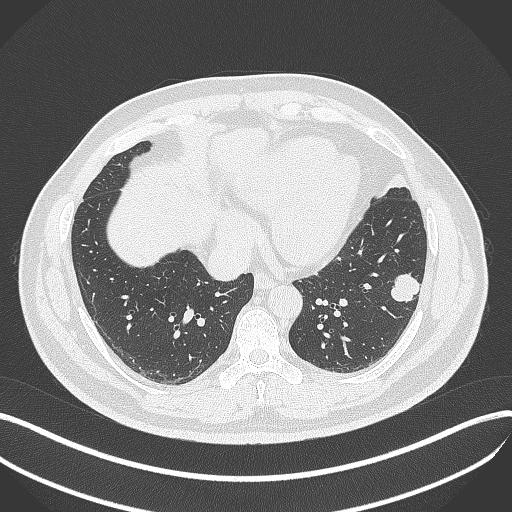
Chest CT, one axial slice. Reconstruction kernel B70f. Lung window (W 1500 / L -600 HU). 1 mm slice thickness. 512 × 512 image matrix, field of view 400 × 400 mm. Patient: male, 39 years. From the clinical record (not read from this slice): clinical TNM (as recorded): T2a N0 M0.
Structures marked on this image (bounding box drawn by a radiologist):
- lung tumour (recorded histology: adenocarcinoma): box from (x=385, y=267) to (x=424, y=305) px